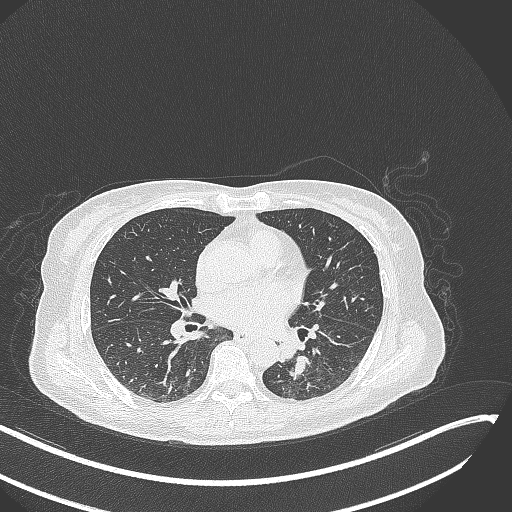
Chest CT, one axial slice; position 128 of 342 along the scan axis; 120 kVp; lung window (W 1500 / L -600 HU); 1 mm slice thickness; 512 × 512 image matrix, field of view 400 × 400 mm. Female patient, age 64 years. Case-level facts recorded for this patient, not image findings: clinical TNM (as recorded): T3 N1 M1; histopathological grade: G3.
Outlined on this slice (rectangle marked by the reading radiologist):
- lung tumour (recorded histology: small cell carcinoma): bounding box <274,339,315,381> (left, top, right, bottom; pixels)